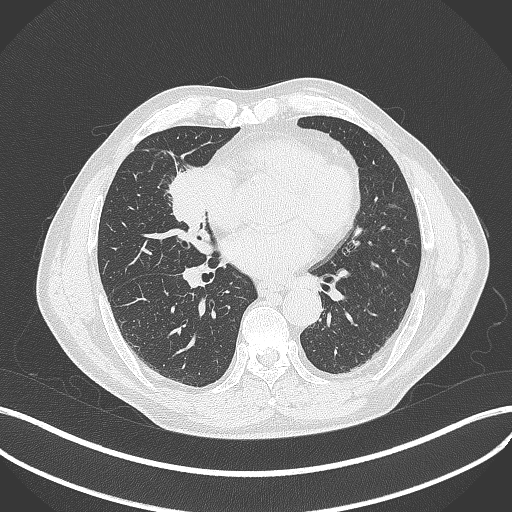
Chest CT, one axial slice. Position 182 of 429 along the scan axis. Reconstruction kernel B70f. 120 kVp. Lung window (W 1500 / L -600 HU). 1 mm slice thickness. 512 × 512 image matrix. Patient: male, 61 years. From the clinical record (not read from this slice): clinical TNM (as recorded): T2b N1 M0.
Outlined on this slice (rectangle marked by the reading radiologist):
- lung tumour (recorded histology: squamous cell carcinoma): bounding box (x1, y1, x2, y2) in pixels: (162, 156, 211, 230)